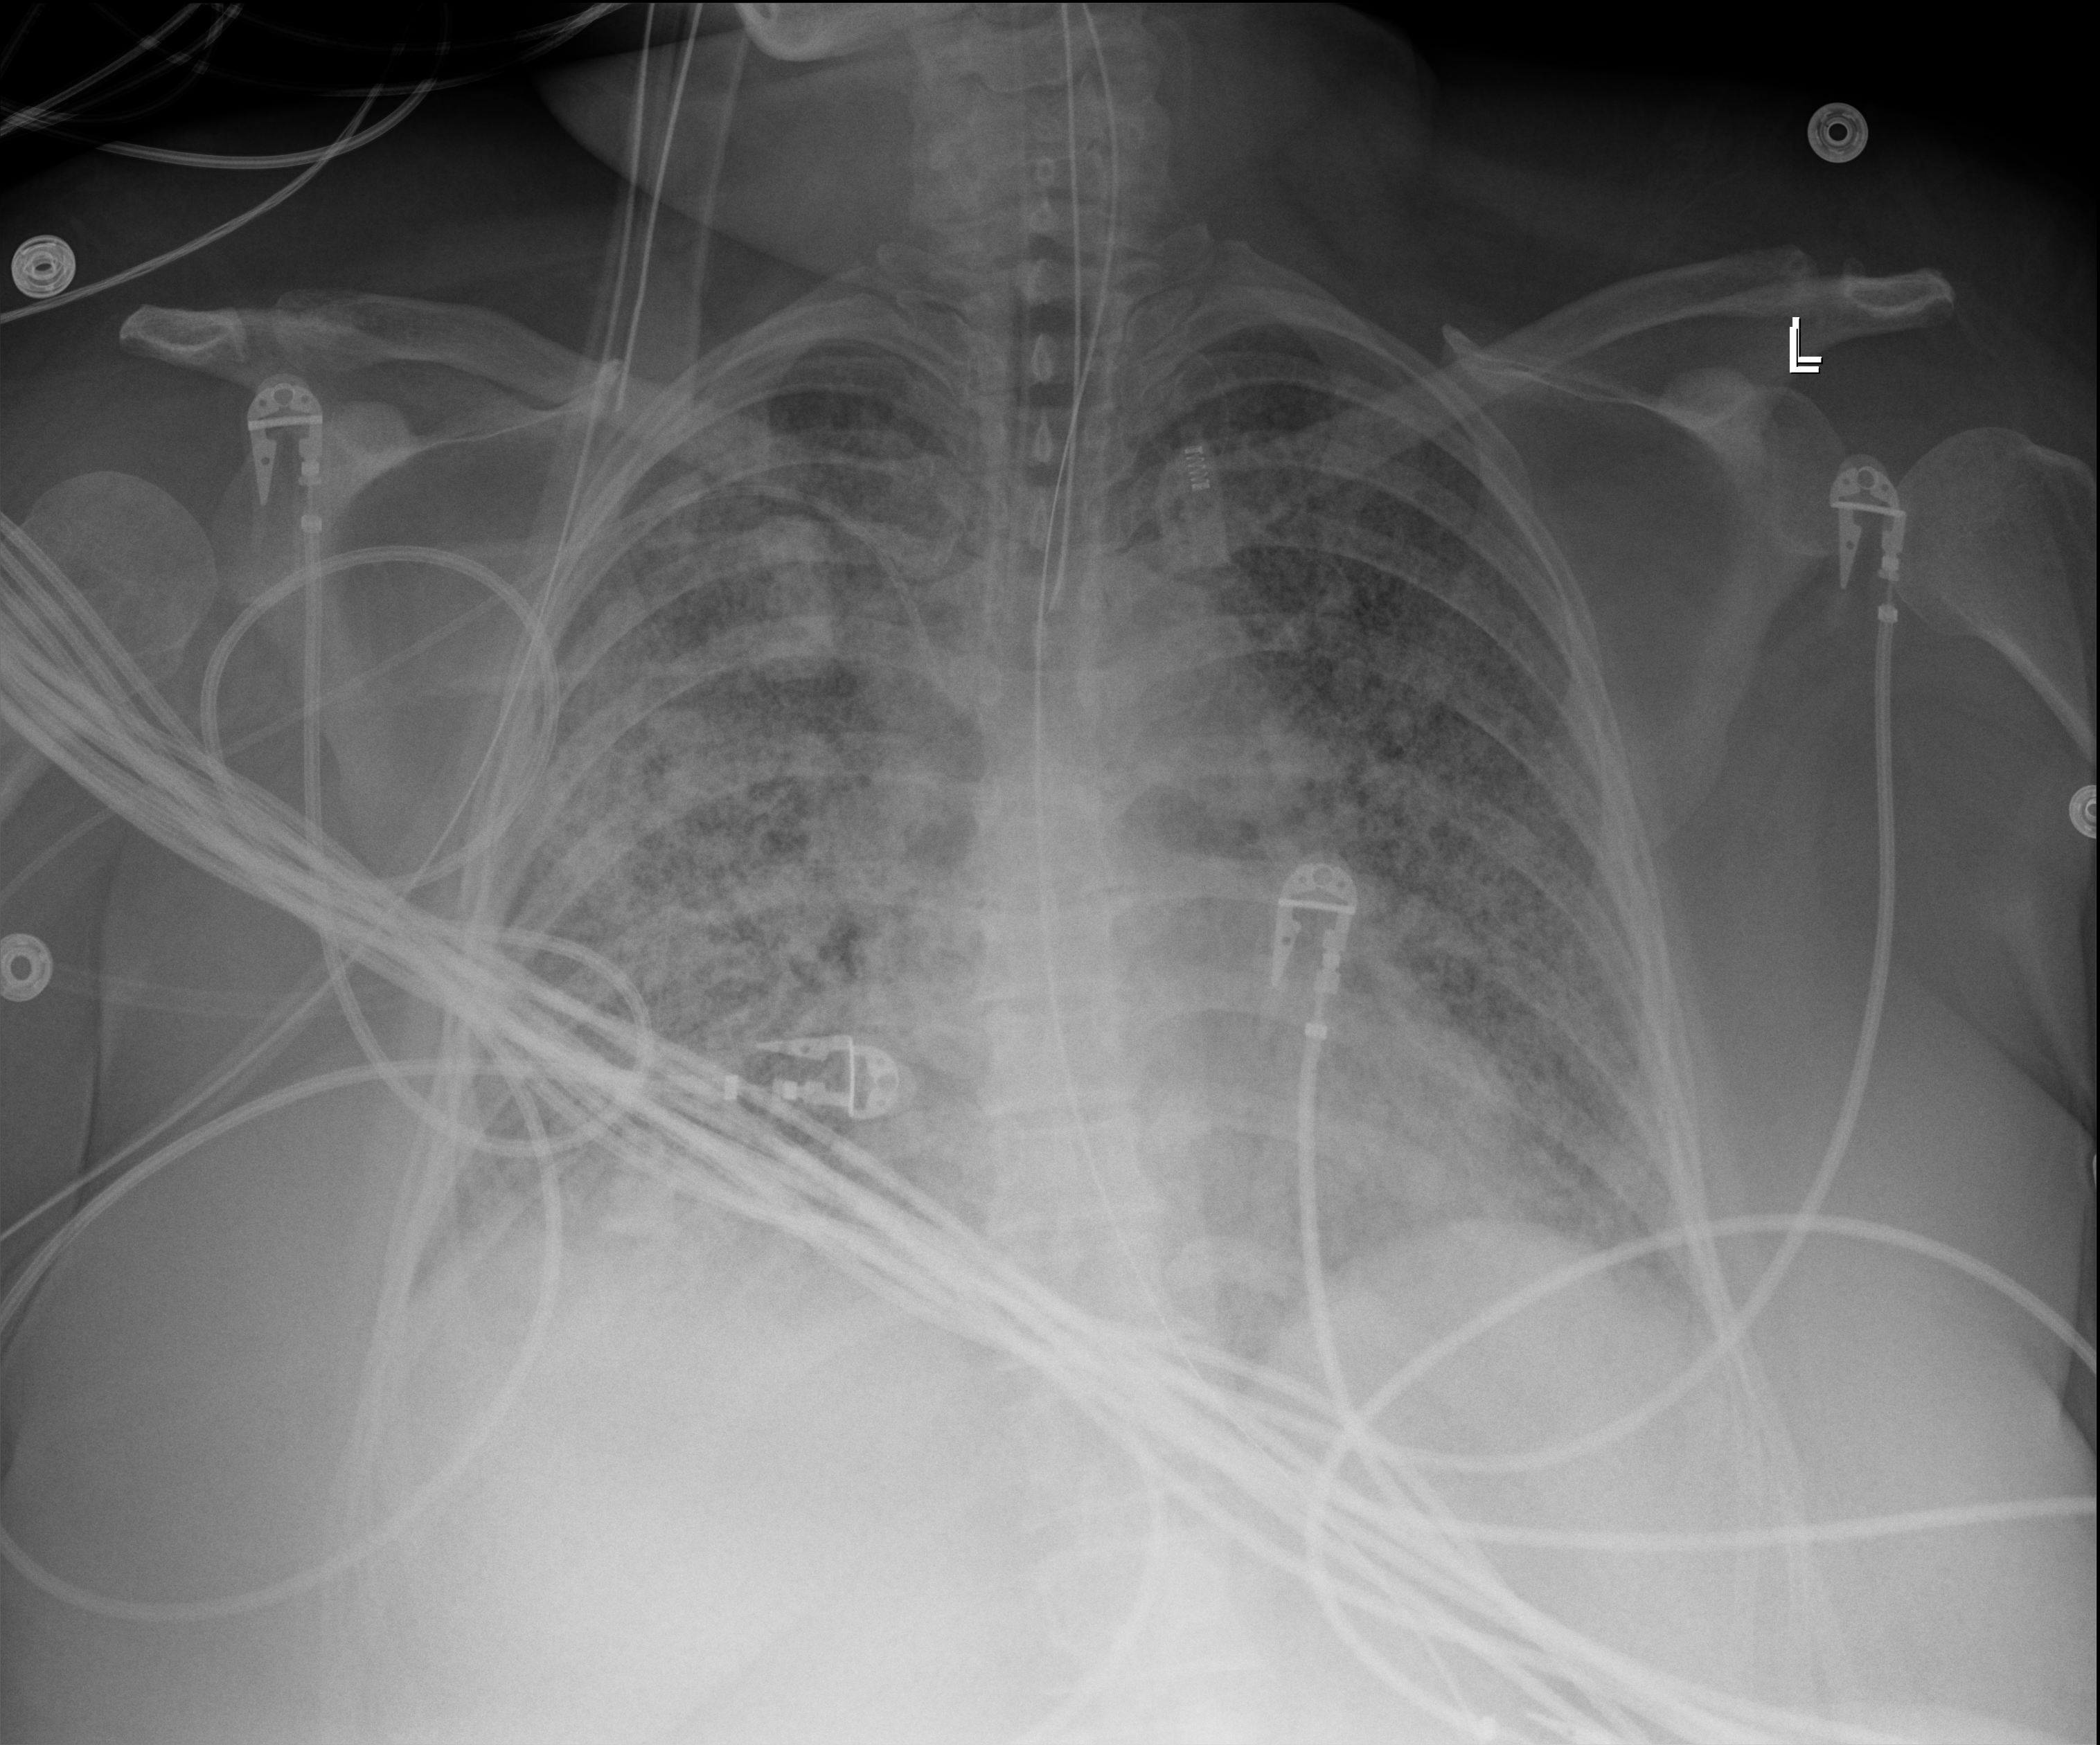
Chest X-ray (portable). Patient hospitalised with COVID-19; female, aged 18–59 years.
Hospital-stay facts (about this admission, not read from this image; timing relative to this image not recorded):
- admitted to intensive care during this hospital stay: yes
- diabetes (admission record): no
- mechanically ventilated during this hospital stay: yes